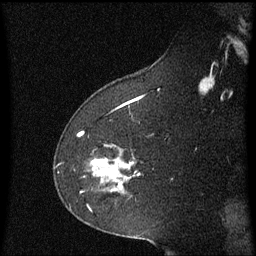
Breast MRI (dynamic contrast-enhanced), one sagittal slice; position 40 of 60 along the scan axis; dynamic contrast-enhanced series, image 2 of 3 at this slice position (ordered by acquisition); 1.5 T; TE 4.2 ms, TR 8.4 ms; 2.2 mm slice thickness; 256 × 256 image matrix, field of view 200 × 200 mm. Patient: female, 60 years. From the clinical record (not read from this slice): setting: breast cancer imaged before/during neoadjuvant chemotherapy; receptor status: triple-negative.
Structures marked on this image (semi-automatically segmented with operator editing):
- analysis volume of interest (the breast-tissue region the enhancement analysis was run in; not a lesion): bounding box (x1, y1, x2, y2) in pixels: (93, 144, 142, 195)
- tumour enhancement mask (voxels above the 70 % enhancement threshold inside the analysis volume of interest): (93, 160, 131, 183)